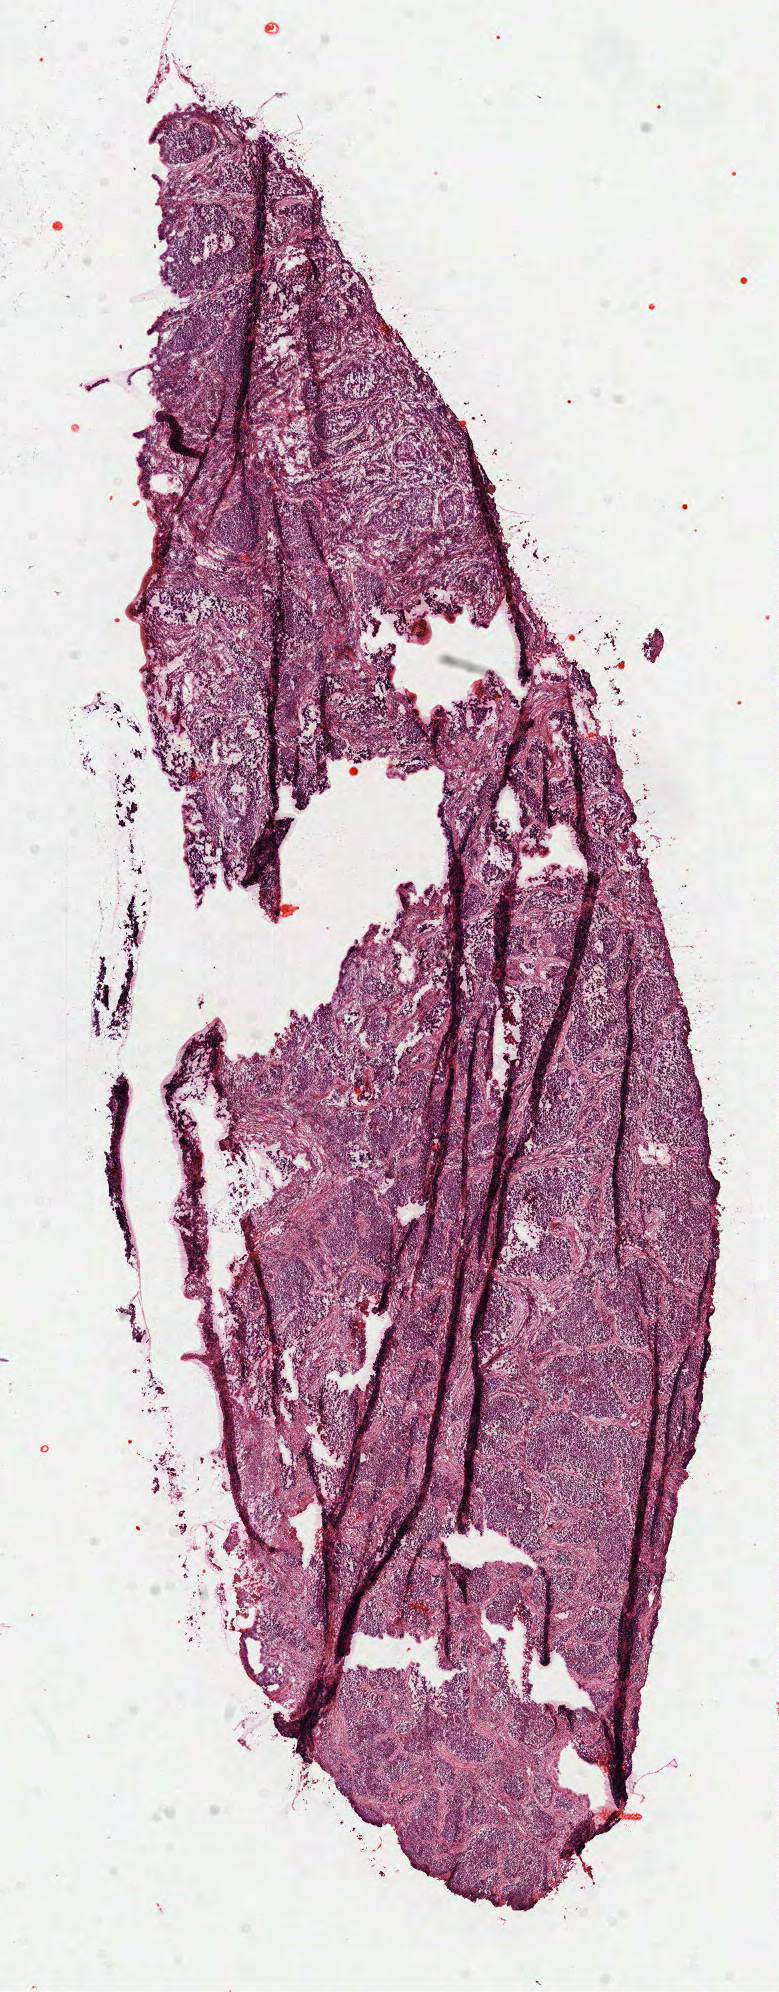
Whole-slide histology image, H&E-stained — a low-resolution overview of the entire scanned area, about 6.3 x 16.1 mm (acquisition: 40x scan); formalin-fixed paraffin-embedded (FFPE) diagnostic section; lung, primary tumour sample. Male patient; age at initial diagnosis 75 years.
Laterality: left. AJCC pathologic stage: IA. Diagnosis: Squamous cell carcinoma, NOS (upper lobe, lung).